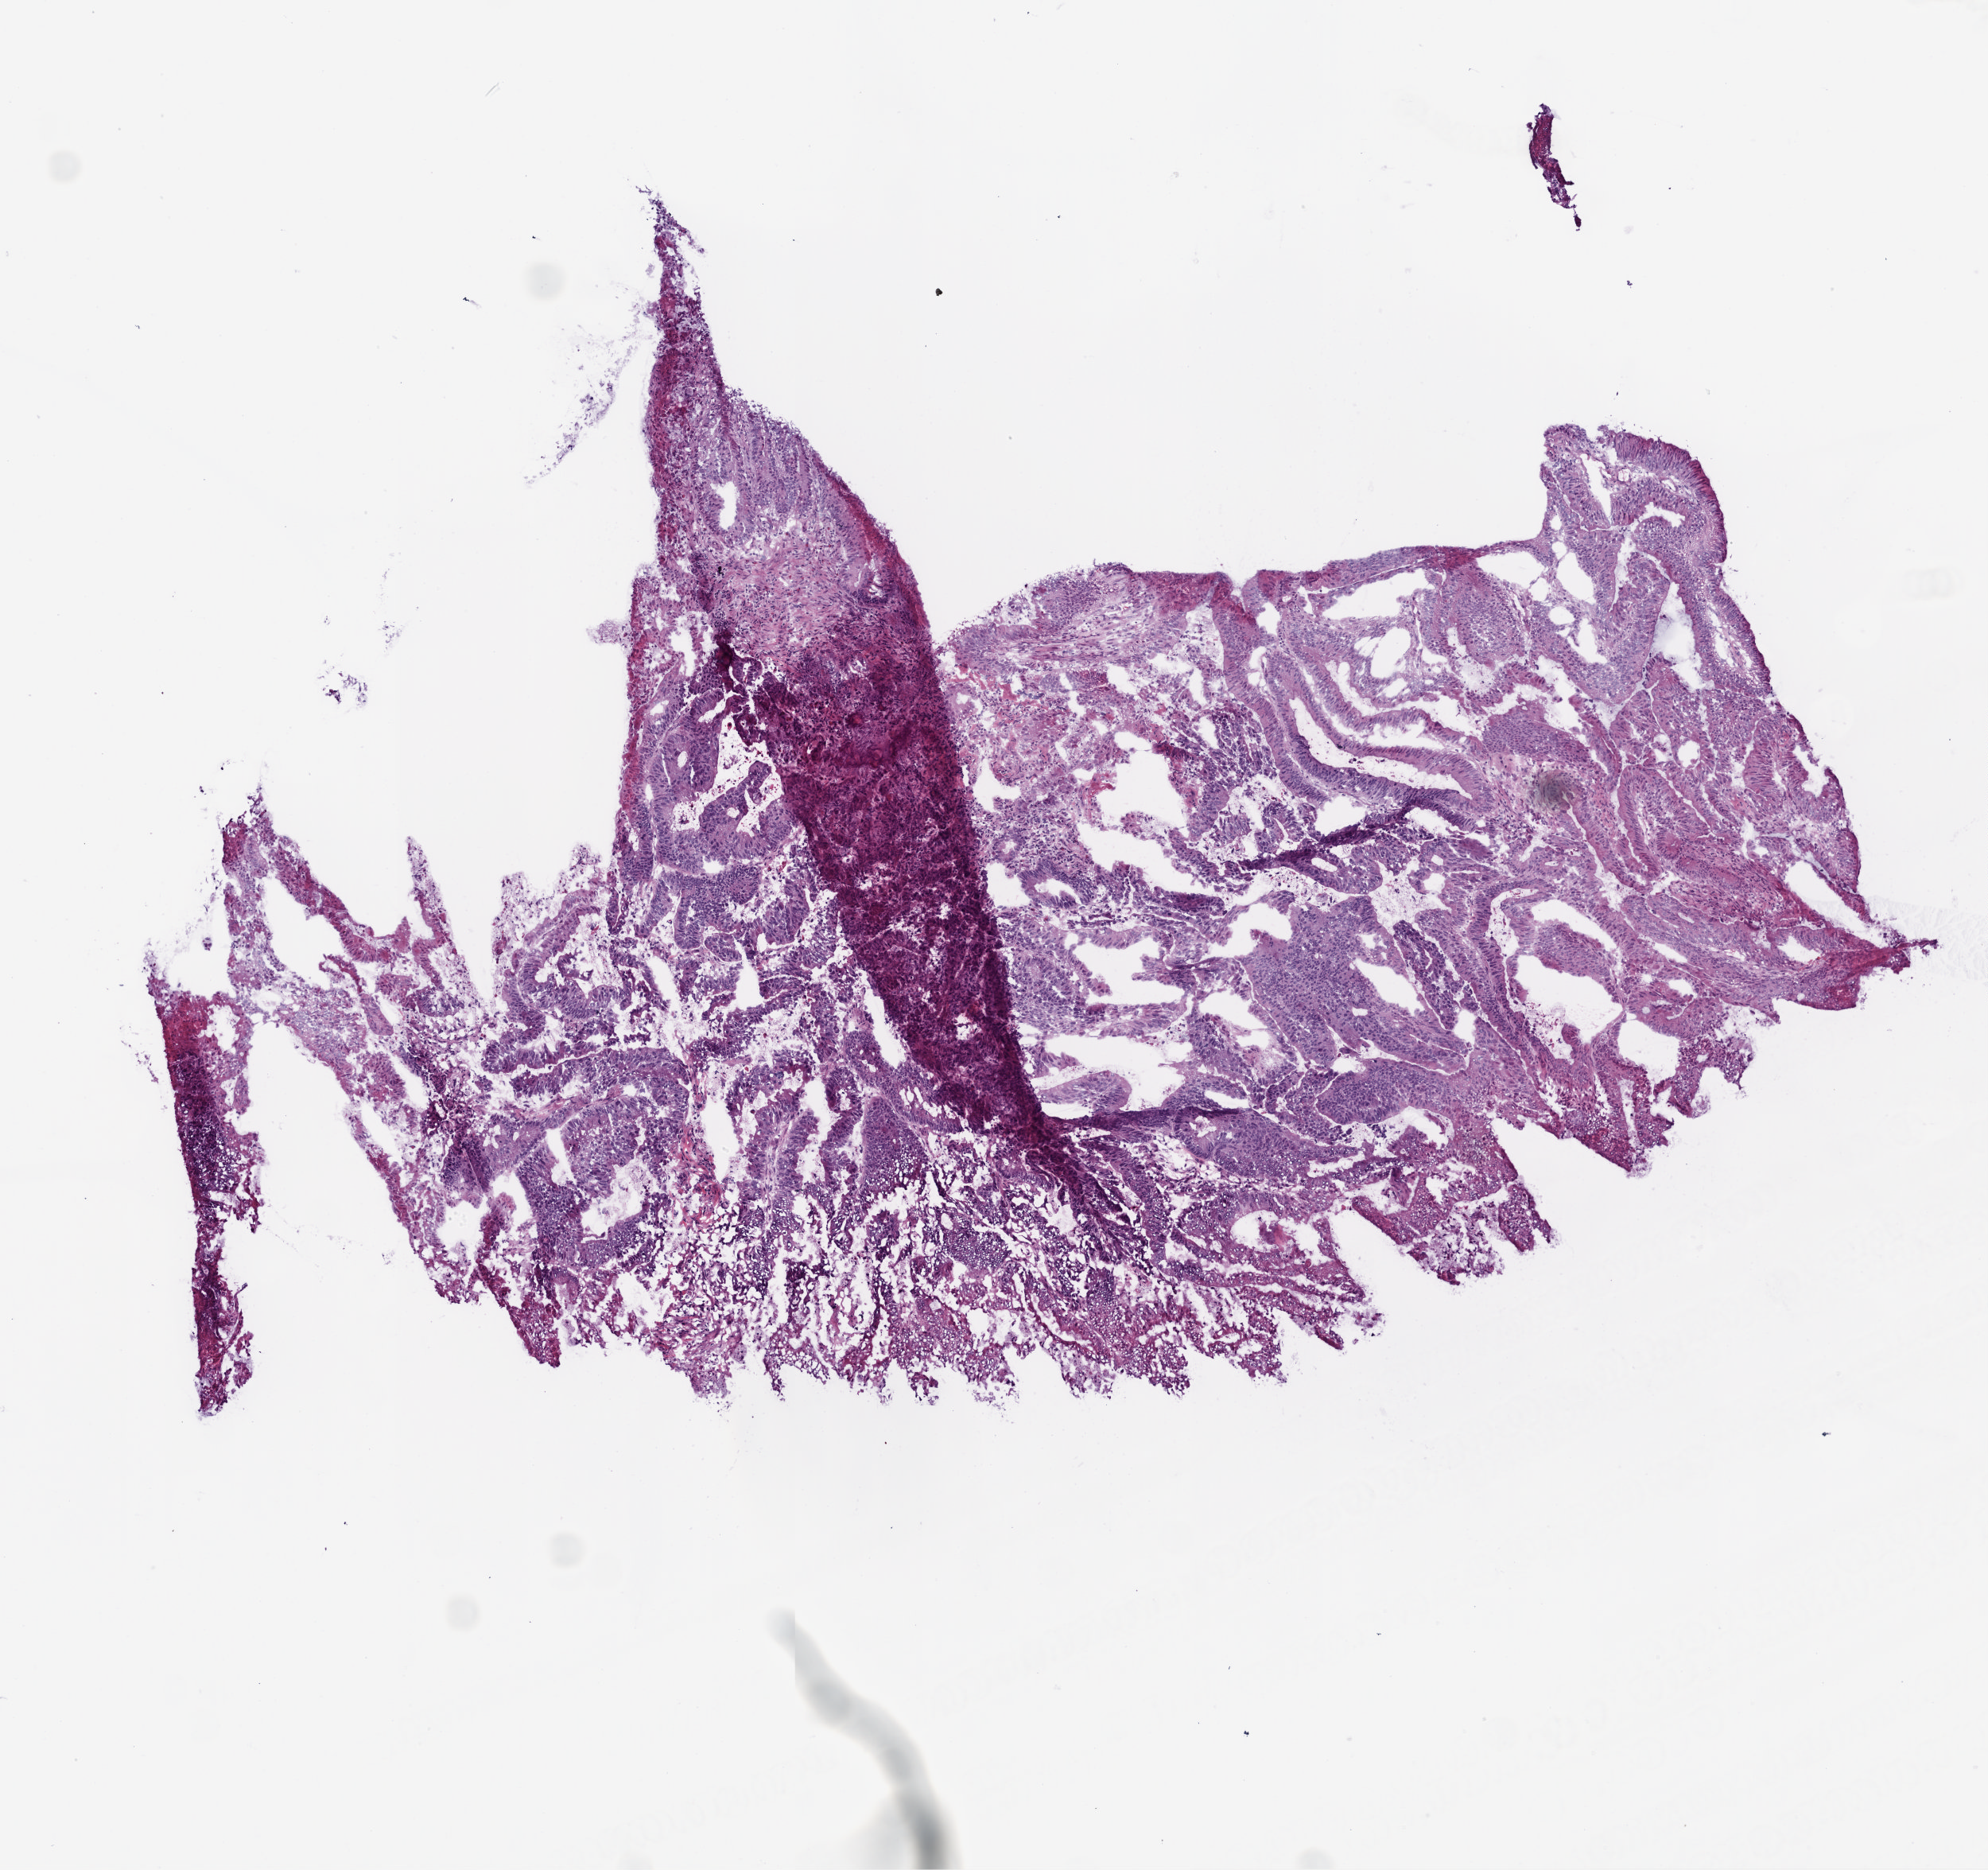
Digitized H&E-stained tissue section (whole slide) — whole scanned area (about 5.0 x 4.7 mm, acquisition: 20x scan) shown as a low-resolution overview, frozen section, sample: primary tumour, colon. Patient: male, age at initial diagnosis 55 years. Slide review estimates, as recorded: tumour cells 80%, tumour nuclei 70%.
Diagnosis: Adenocarcinoma, NOS.